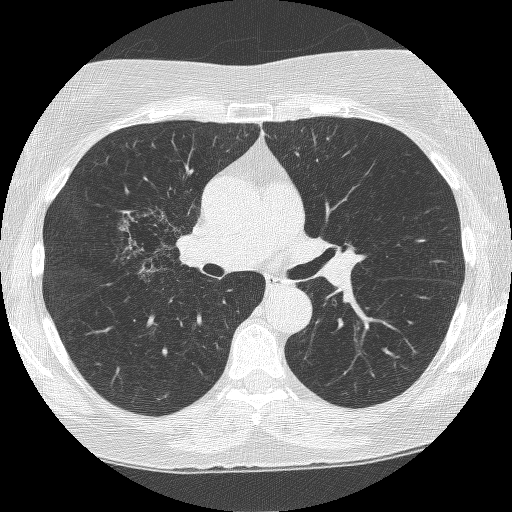
Chest CT (low-dose screening protocol), one axial image. Second annual screen. Lung window (W 1500 / L -600 HU). 1.25 mm slice thickness. Lung (sharp) reconstruction kernel (BONE). 120 kVp. Slice 143 of 249 in the series. Female, age 64 years at enrolment.
Lesion marked by an expert reader, bounding box <116,205,202,287> (left, top, right, bottom; pixels). The screening reader recorded 4 non-calcified nodules or masses ≥4 mm on this exam (right upper lobe, right upper lobe, right upper lobe, left upper lobe); which of them this box marks is not recorded. Participant outcome: lung cancer diagnosed 381 days after this screen (after the third annual screen) — adenocarcinoma, NOS, right upper lobe, right middle lobe, right hilum, stage IV (AJCC 6th edition), 85 mm at pathology.